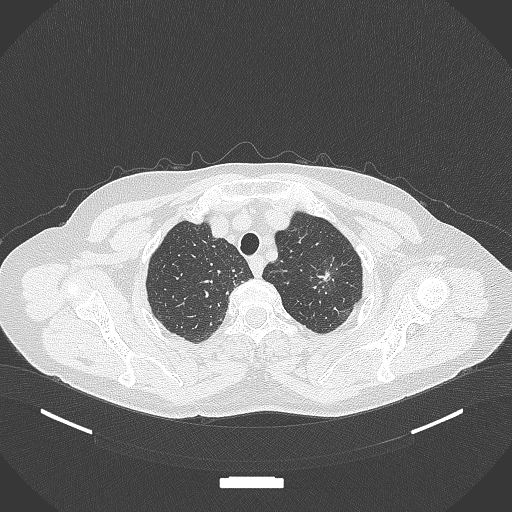
Chest CT, one axial slice. Position 311 of 369 along the scan axis. Reconstruction kernel B70f. 120 kVp. Lung window (W 1500 / L -600 HU). 1 mm slice thickness. 512 × 512 image matrix. Female patient, age 64 years. Case-level facts recorded for this patient, not image findings: clinical TNM (as recorded): T1c N0 M0.
Outlined on this slice (bounding box drawn by a radiologist):
- lung tumour (recorded histology: adenocarcinoma): box from (x=306, y=254) to (x=349, y=298) px